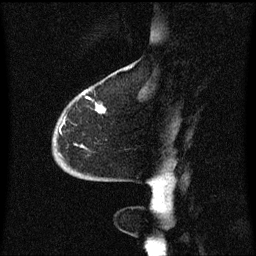
Breast MRI (dynamic contrast-enhanced), one sagittal slice; position 16 of 60 along the scan axis; dynamic contrast-enhanced series, image 2 of 3 at this slice position (ordered by acquisition); 1.5 T; TE 4.2 ms, TR 8.4 ms; 2 mm slice thickness; 256 × 256 image matrix, field of view 200 × 200 mm. Patient: female, 68 years. From the clinical record (not read from this slice): setting: breast cancer imaged before/during neoadjuvant chemotherapy; receptor status: triple-negative.
Outlined on this slice (semi-automatically segmented with operator editing):
- analysis volume of interest (the breast-tissue region the enhancement analysis was run in; not a lesion): bounding box <54,94,107,173> (left, top, right, bottom; pixels)
- tumour enhancement mask (voxels above the 70 % enhancement threshold inside the analysis volume of interest): <97,104,106,113>